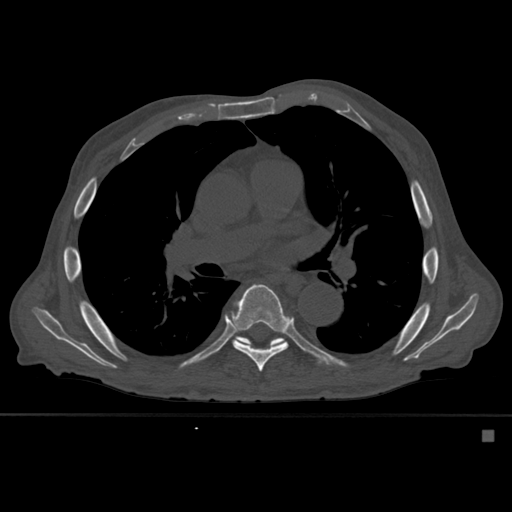
CT including the spine, one axial slice. Position 365 of 527 along the scan axis. Bone window (W 1800 / L 400 HU). 1.5 mm slice thickness. 512 × 512 image matrix, field of view 373 × 373 mm. Male patient, age 78 years. Case-level facts recorded for this patient, not image findings: primary cancer: prostate.
Outlined on this slice (semi-automatic segmentation, software-assisted and operator-edited):
- T7 vertebra: box from (x=229, y=284) to (x=291, y=372) px
- T8 vertebra: (x=236, y=336)–(x=285, y=347)